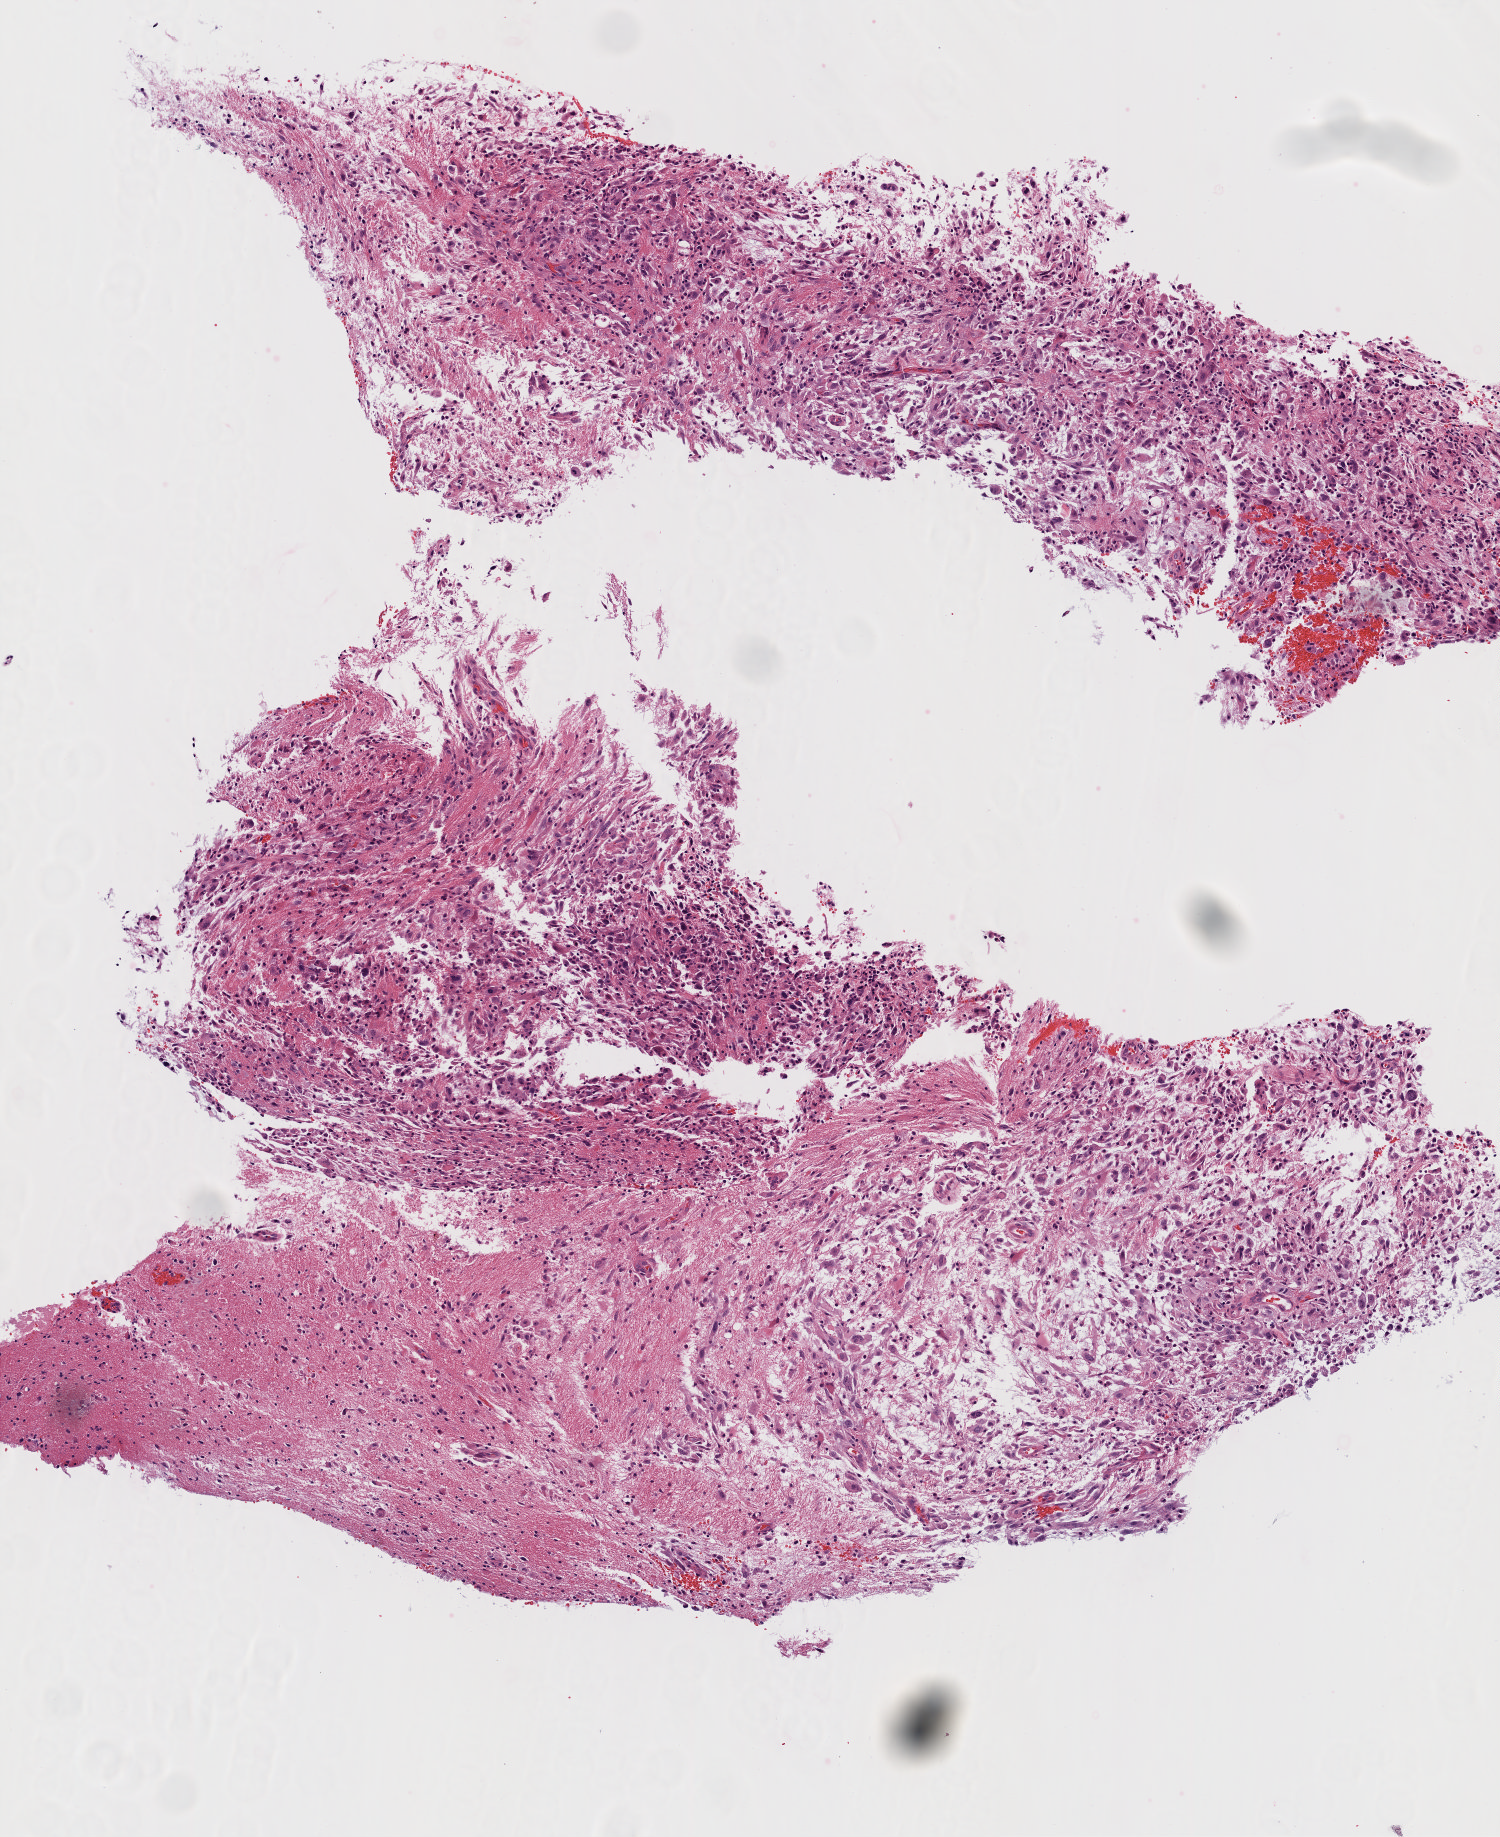
Digitized H&E-stained tissue section (whole slide), low-resolution overview of the scanned area, about 3.0 x 3.7 mm; FFPE section; sample: primary tumour, brain. Male, age 54 years at initial diagnosis.
Pathologic diagnosis: Glioblastoma.